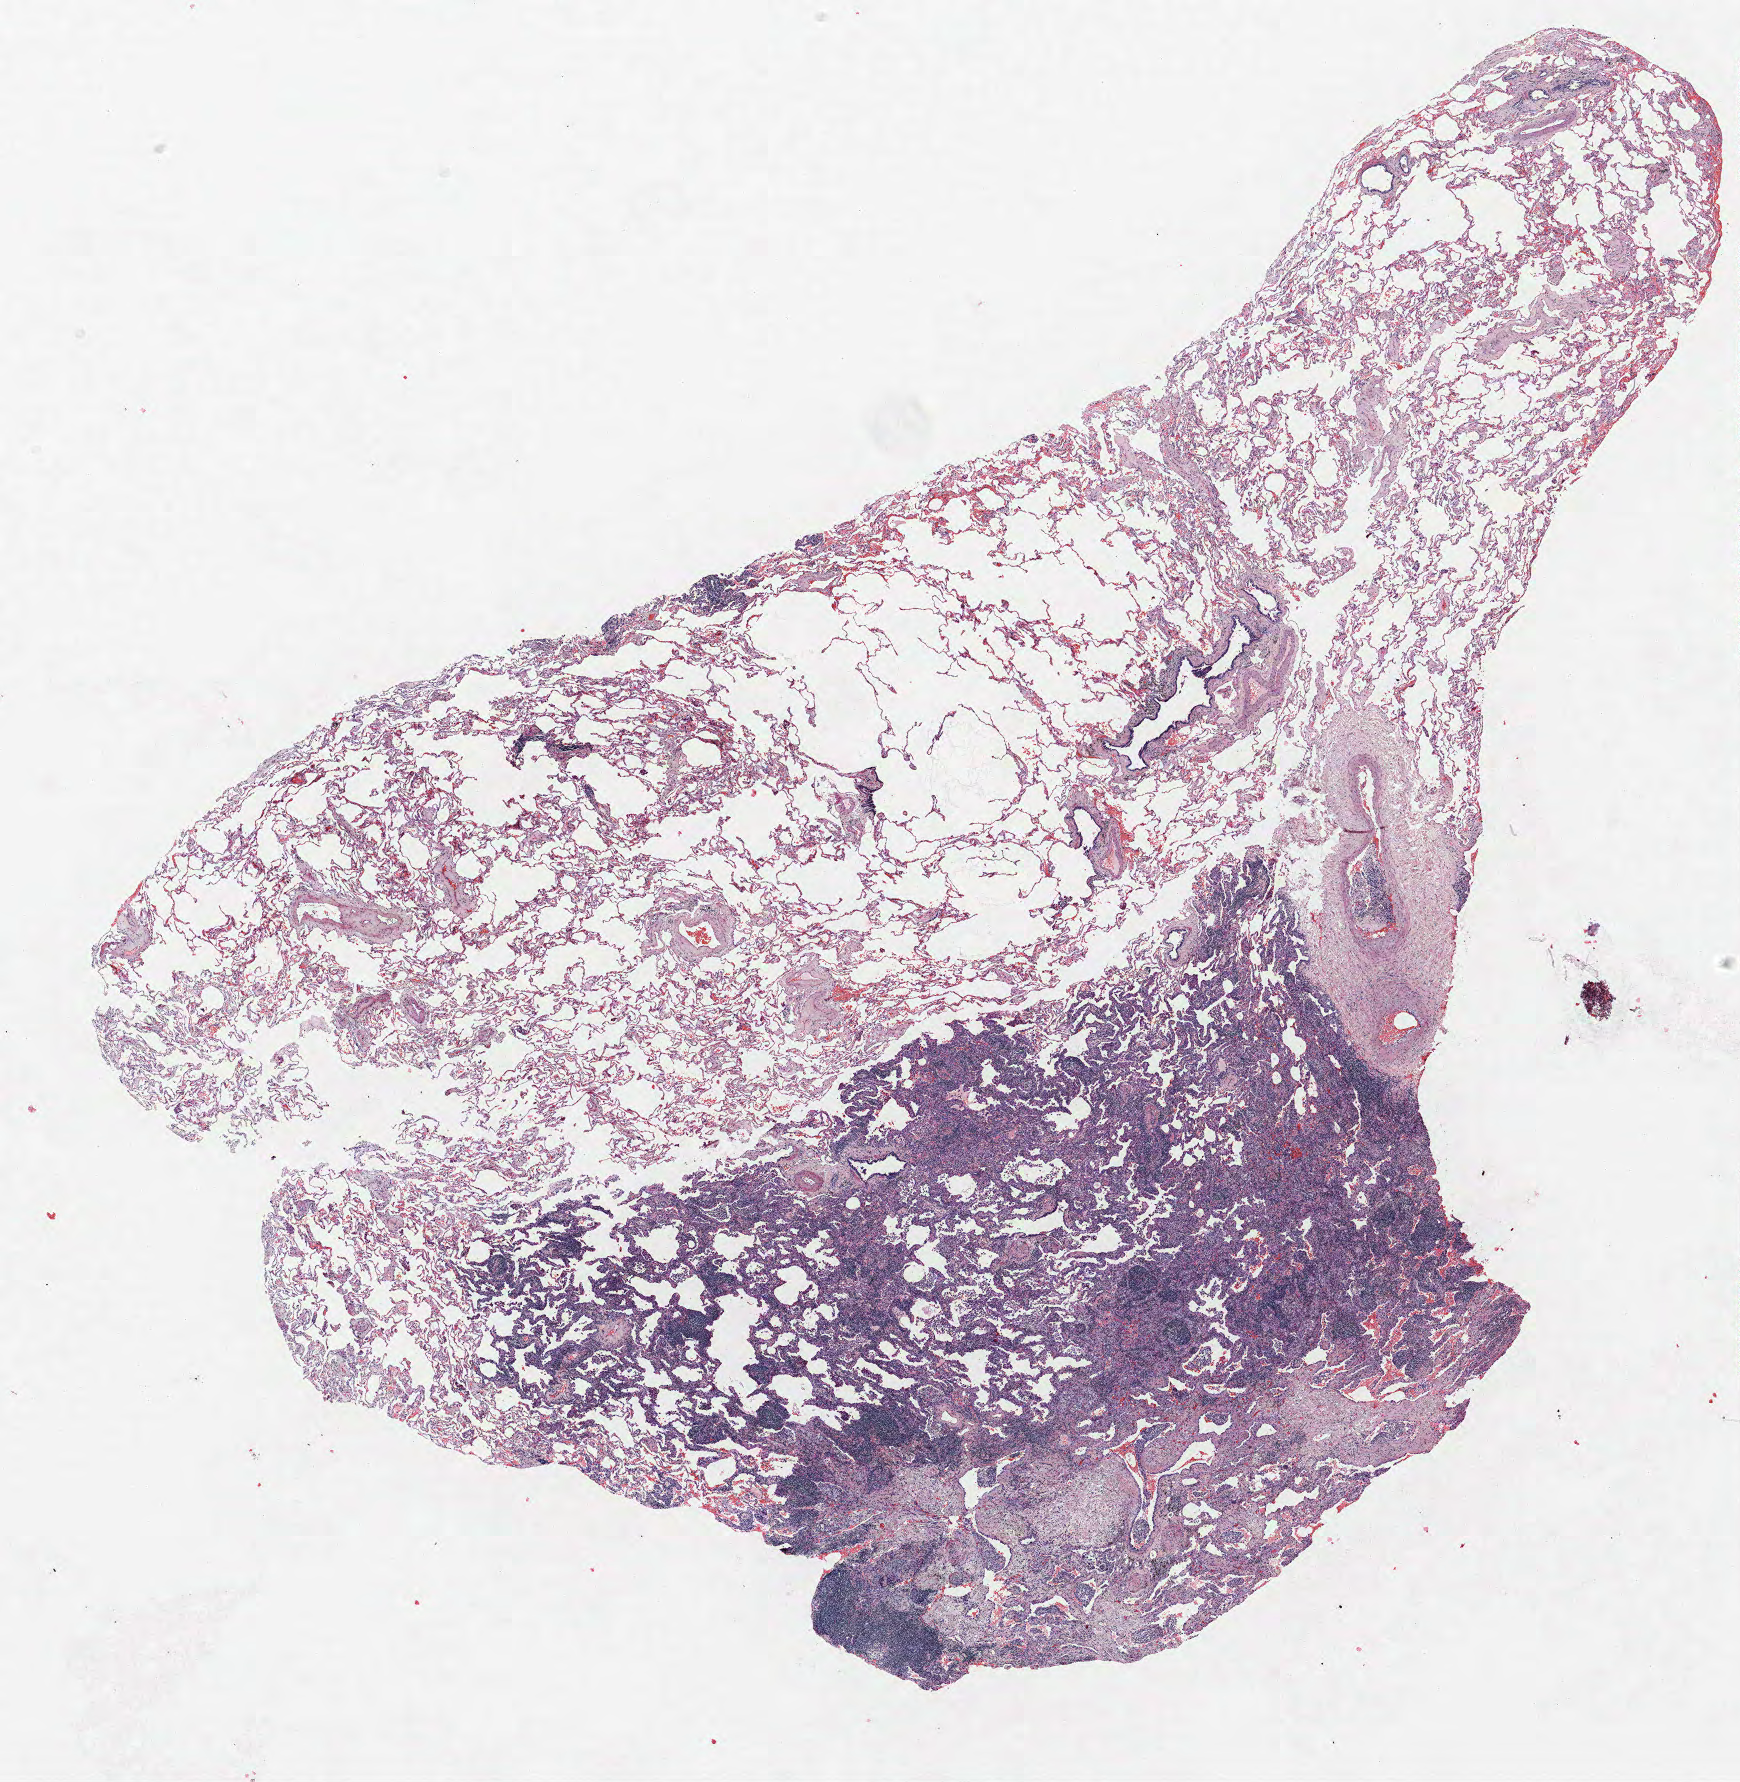
H&E-stained whole-slide image — a low-resolution overview of the entire scanned area, about 13.9 x 14.3 mm (acquisition: 40x scan); formalin-fixed paraffin-embedded (FFPE) section; lung. Female patient, aged 71 at enrolment. Former smoker at enrolment. Grade: moderately differentiated (G2).
Tumour size (pathology): 12 mm. Participant's lung-cancer diagnosis: Adenocarcinoma, NOS (ICD-O-3 8140/3). Primary tumour location (clinical record): left upper lobe. Stage (AJCC 6th edition): IIA.